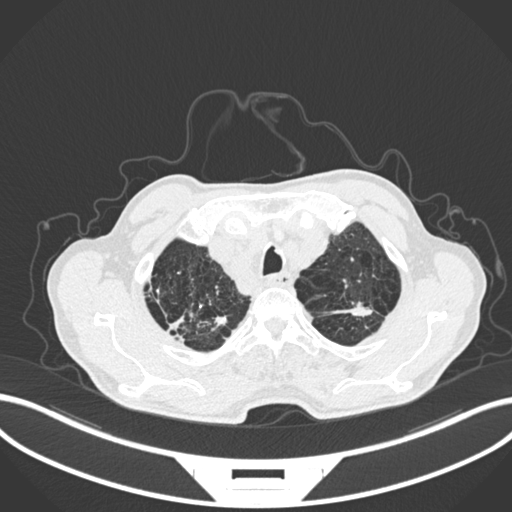
Chest CT, one axial slice. Position 243 of 287 along the scan axis. Reconstruction kernel B30f. Lung window (W 1500 / L -600 HU). 1 mm slice thickness. 512 × 512 image matrix. Male patient, age 74 years. From the clinical record (not read from this slice): clinical TNM (as recorded): T2a N1 M0.
Annotated regions visible in this slice (rectangle marked by the reading radiologist):
- lung tumour (recorded histology: adenocarcinoma): box from (x=337, y=303) to (x=373, y=319) px